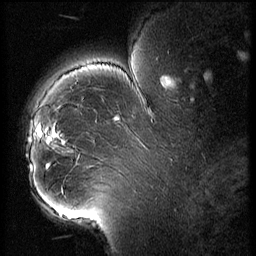
Breast MRI (dynamic contrast-enhanced), one sagittal slice. Slice 44 of 56 in the series (ordered by position). 3 images stored at this slice position (order not interpretable as contrast timing). 1.5 T. TE 4.2 ms, TR 9 ms. 256 × 256 image matrix, field of view 180 × 180 mm. Patient: female, 43 years. From the clinical record (not read from this slice): setting: breast cancer imaged before/during neoadjuvant chemotherapy; receptor status: HER2-positive.
Outlined on this slice (semi-automatic segmentation, software-assisted and operator-edited):
- analysis volume of interest (the breast-tissue region the enhancement analysis was run in; not a lesion): box from (x=25, y=92) to (x=74, y=211) px
- tumour enhancement mask (voxels above the 140 % enhancement threshold inside the analysis volume of interest): (x=38, y=127)–(x=59, y=143)